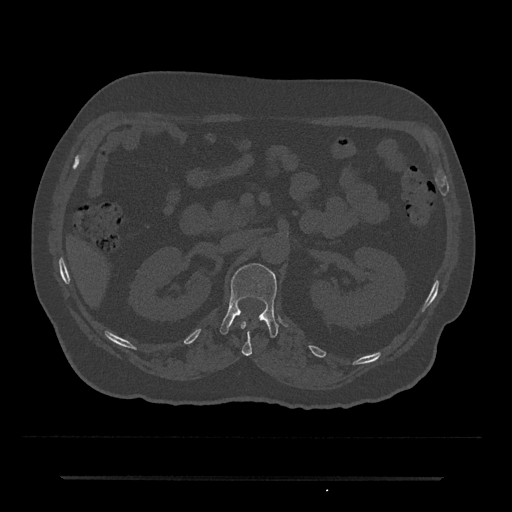
CT including the spine, one axial slice. Position 87 of 797 along the scan axis. Reconstruction kernel Br40s/3. 120 kVp. Bone window (W 1800 / L 400 HU). 0.5 mm slice thickness. 512 × 512 image matrix, field of view 437 × 437 mm. Male patient, age 69 years. Case-level facts recorded for this patient, not image findings: primary cancer: prostate.
Annotated regions visible in this slice (semi-automatically segmented with operator editing):
- L1 vertebra: bounding box <219,263,278,338> (left, top, right, bottom; pixels)
- T12 vertebra: <240,320,264,356>